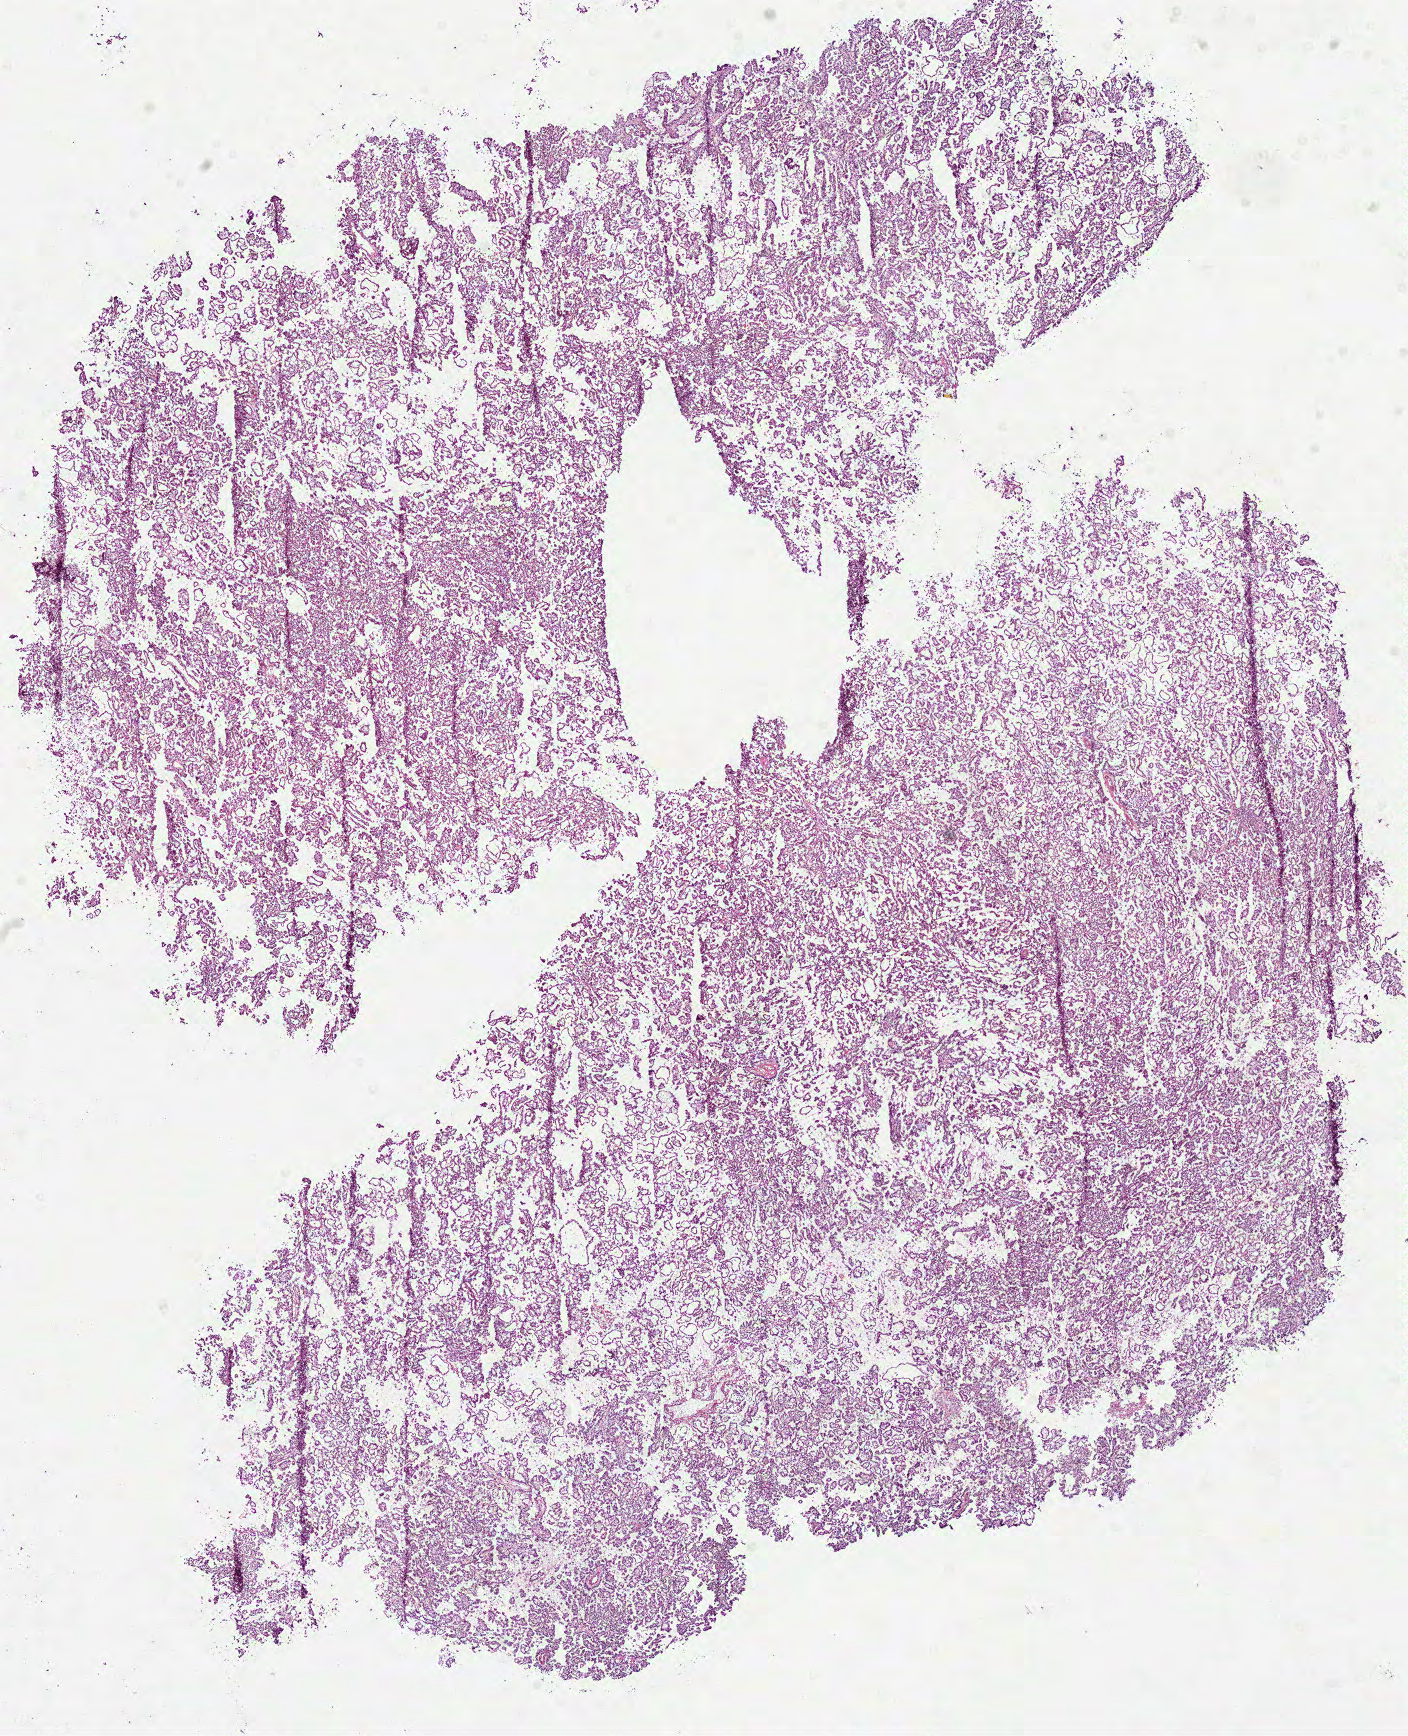
H&E whole-slide image — a low-resolution overview of the entire scanned area, about 11.4 x 14.0 mm (acquisition: 40x scan), frozen section, primary tumour sample from the kidney. Male, age 60 years at initial diagnosis. Composition of this section per pathologist review: tumour cells 100%, tumour nuclei 90%, normal cells 0%, stromal cells 0%, necrosis 0%. Infiltration values recorded for this section: lymphocyte infiltration 0%, monocyte infiltration 0%, neutrophil infiltration 0%.
• pathologic diagnosis: Papillary adenocarcinoma, NOS
• laterality: right
• AJCC pathologic stage: I (7th edition)